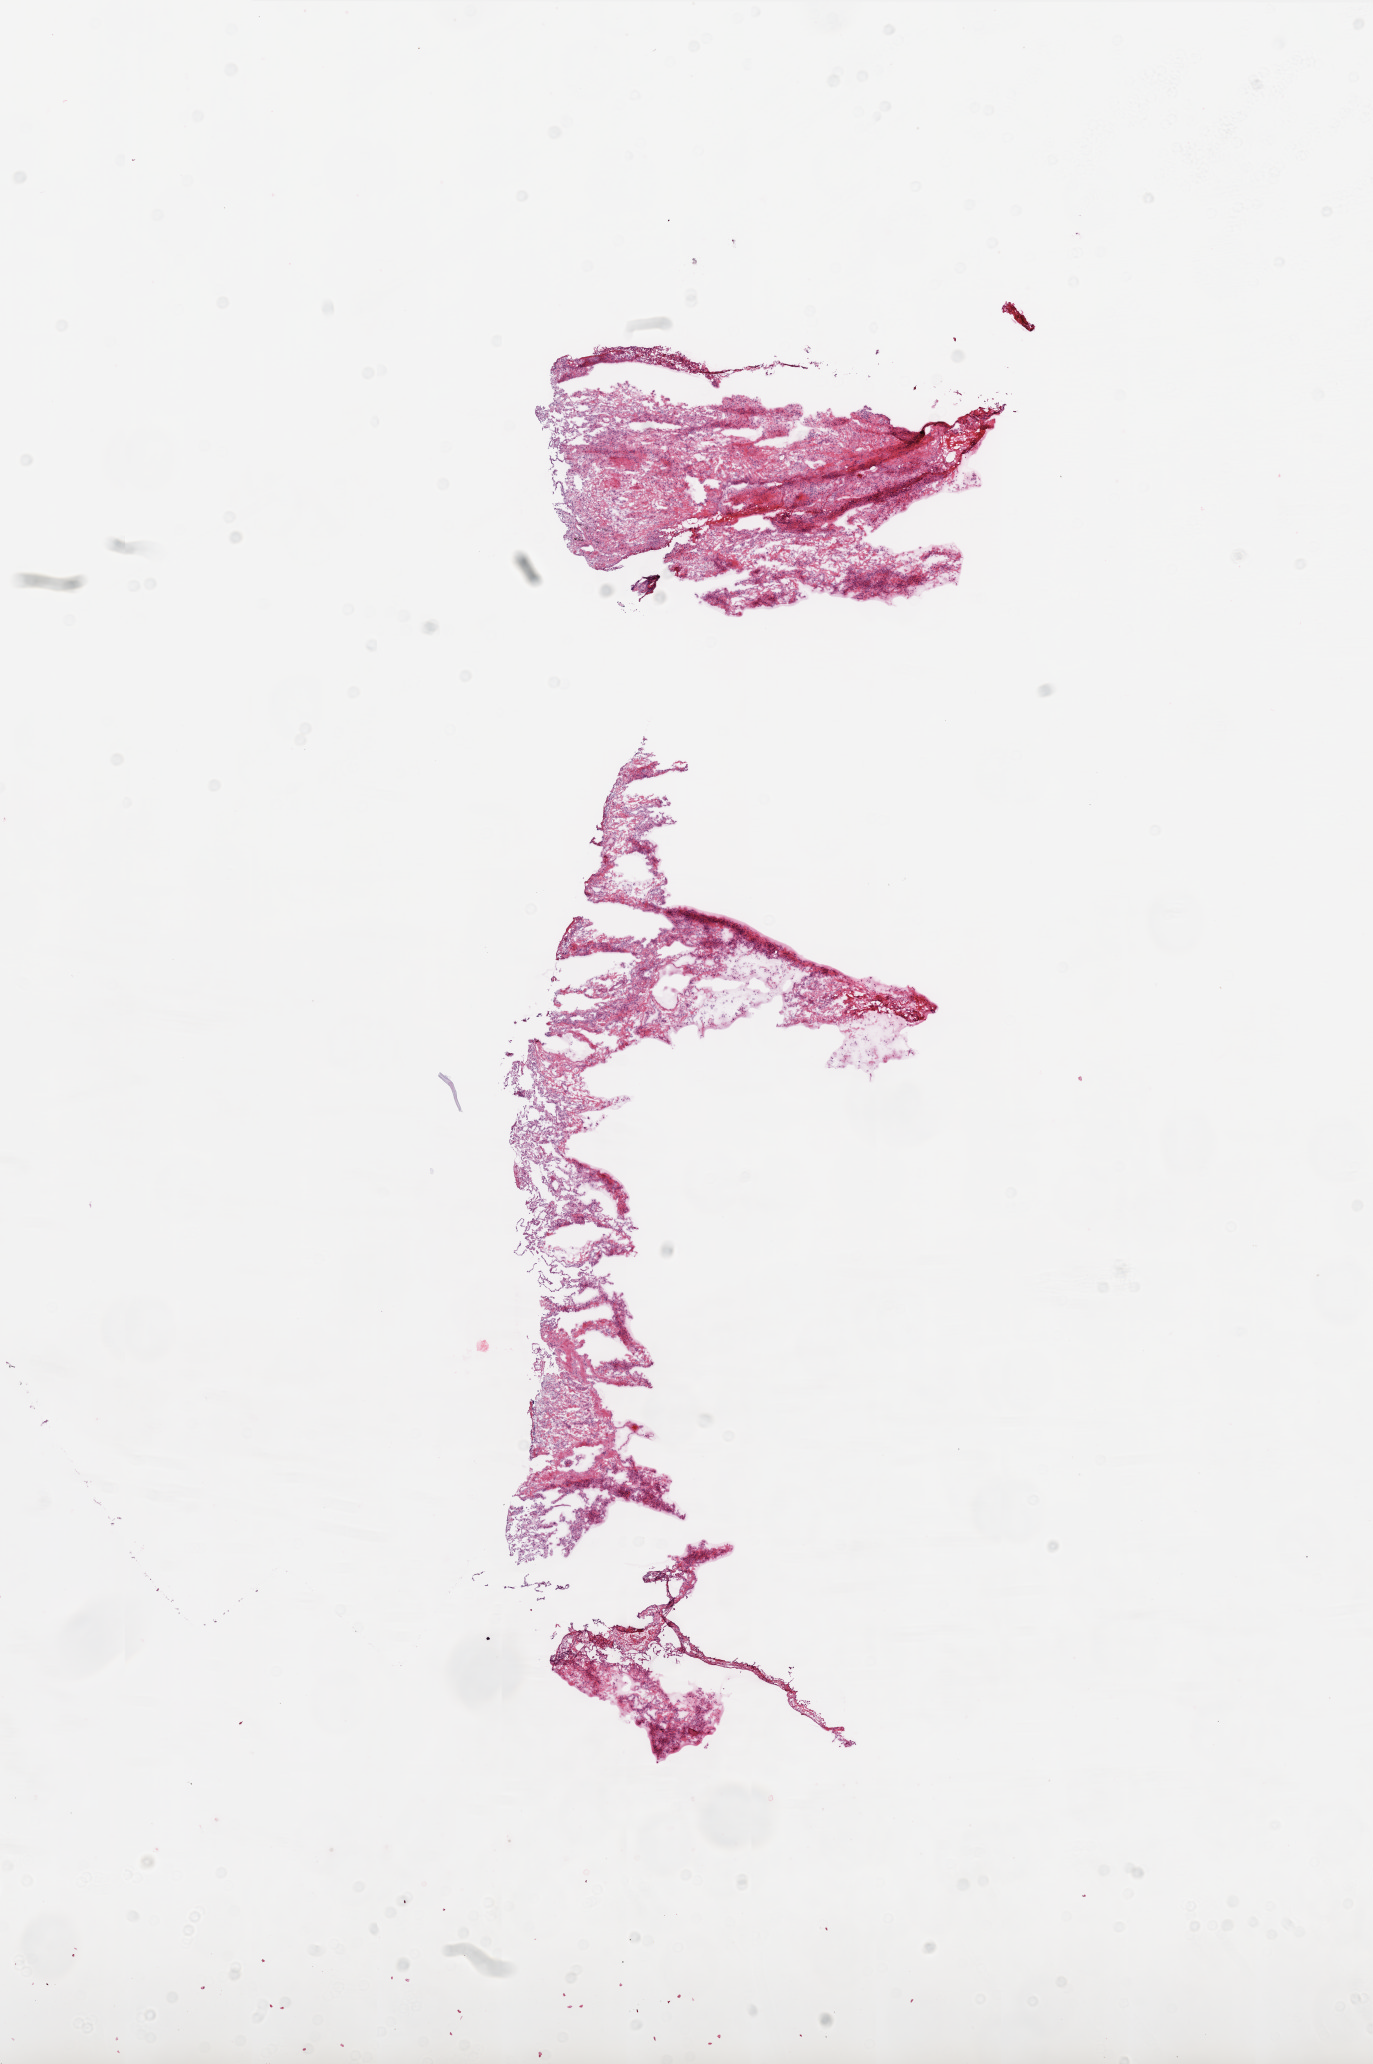
Hematoxylin and eosin (H&E) stained whole-slide image, whole scanned area (about 11.0 x 16.5 mm, acquisition: 20x scan) shown as a low-resolution overview. Frozen section from the bottom of the tissue portion. Solid tissue normal (non-tumour tissue) sample from the lung. Male, age 71 years at initial diagnosis.
This section: solid tissue normal (non-tumour) sample from the same patient. Patient diagnosis: Squamous cell carcinoma, NOS.